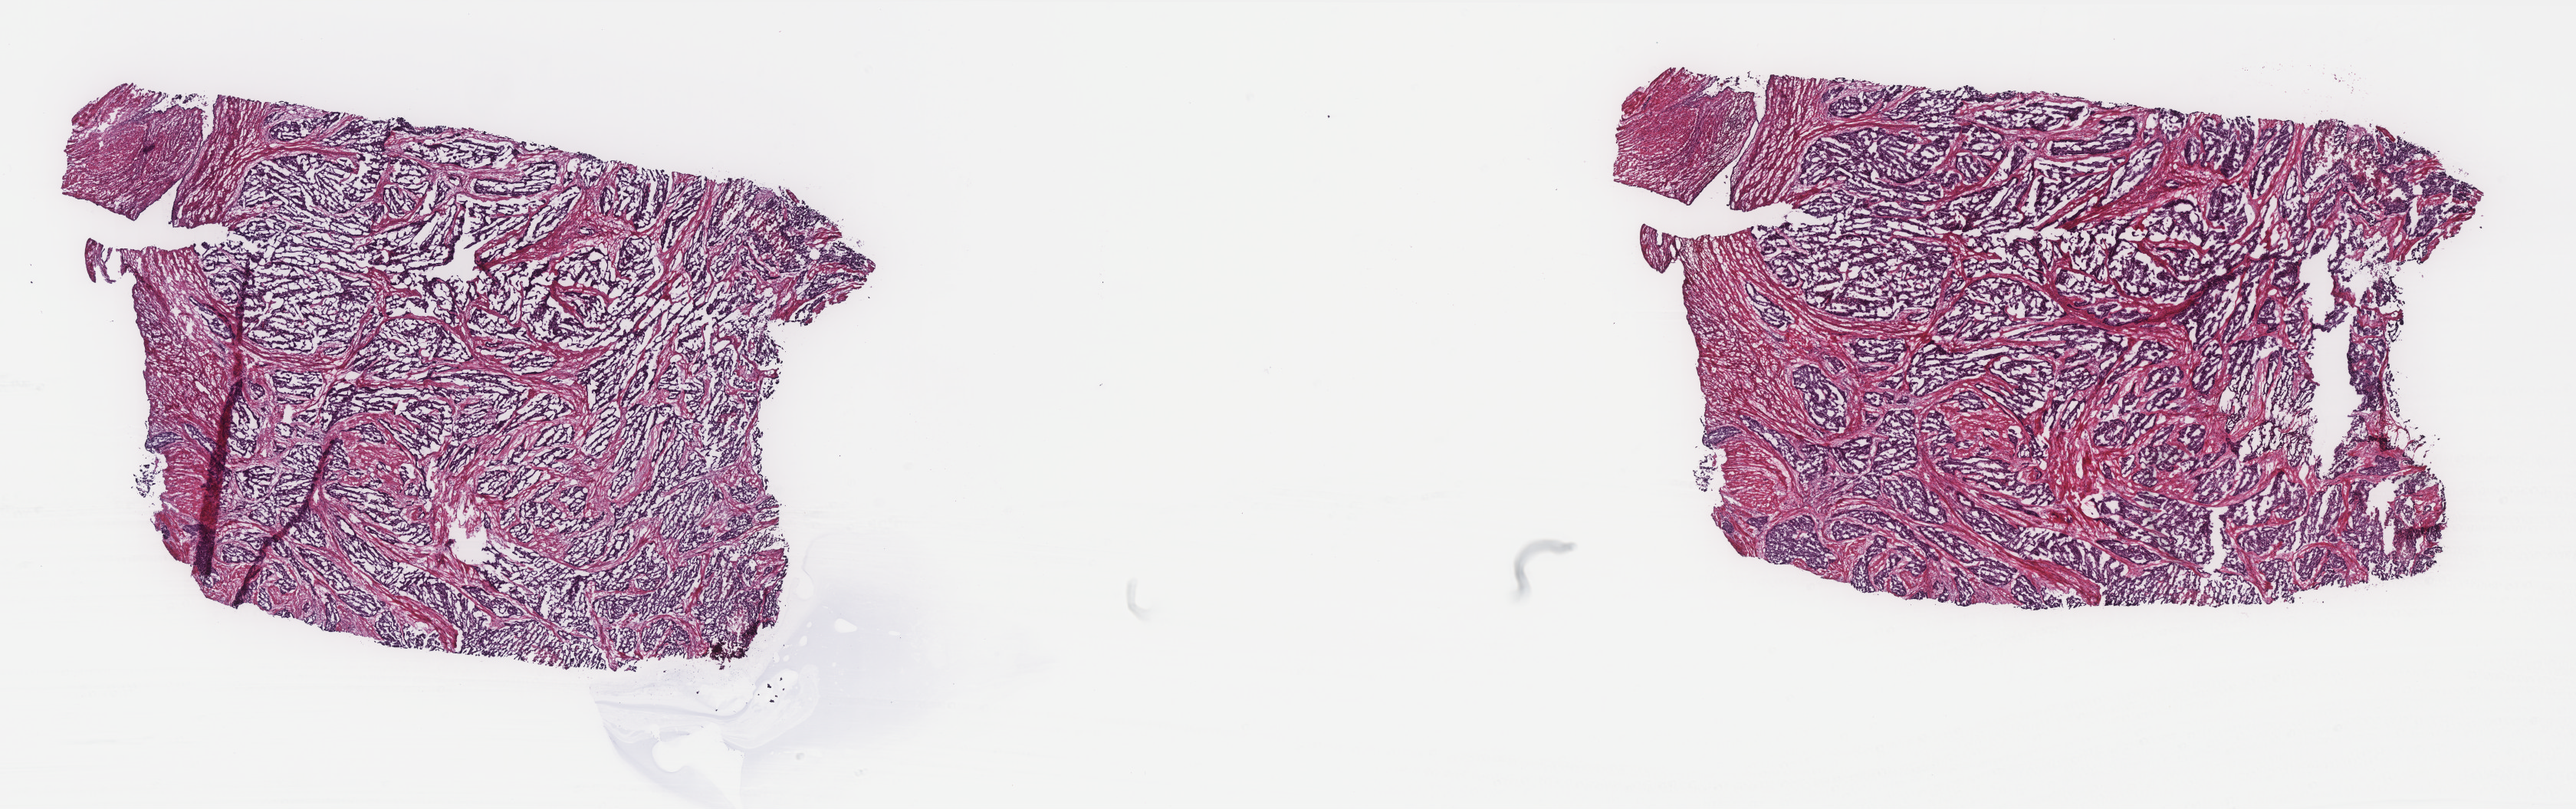
Whole-slide histology image, Hematoxylin and eosin (H&E) stained — a low-resolution overview of the entire scanned area, about 26.9 x 8.5 mm (acquisition: 40x scan). Frozen section. Primary tumour sample from the uterus. Female patient; age at initial diagnosis 54 years. Histologic grade: G2 (moderately differentiated). Composition of this section per pathologist review: tumour cells 80%, tumour nuclei 75%, normal cells 0%, stromal cells 20%, necrosis 0%. Infiltration values recorded for this section: lymphocyte infiltration 0%, monocyte infiltration 0%, neutrophil infiltration 0%.
Pathologic diagnosis: Endometrioid adenocarcinoma, NOS (endometrium). FIGO stage: IB.